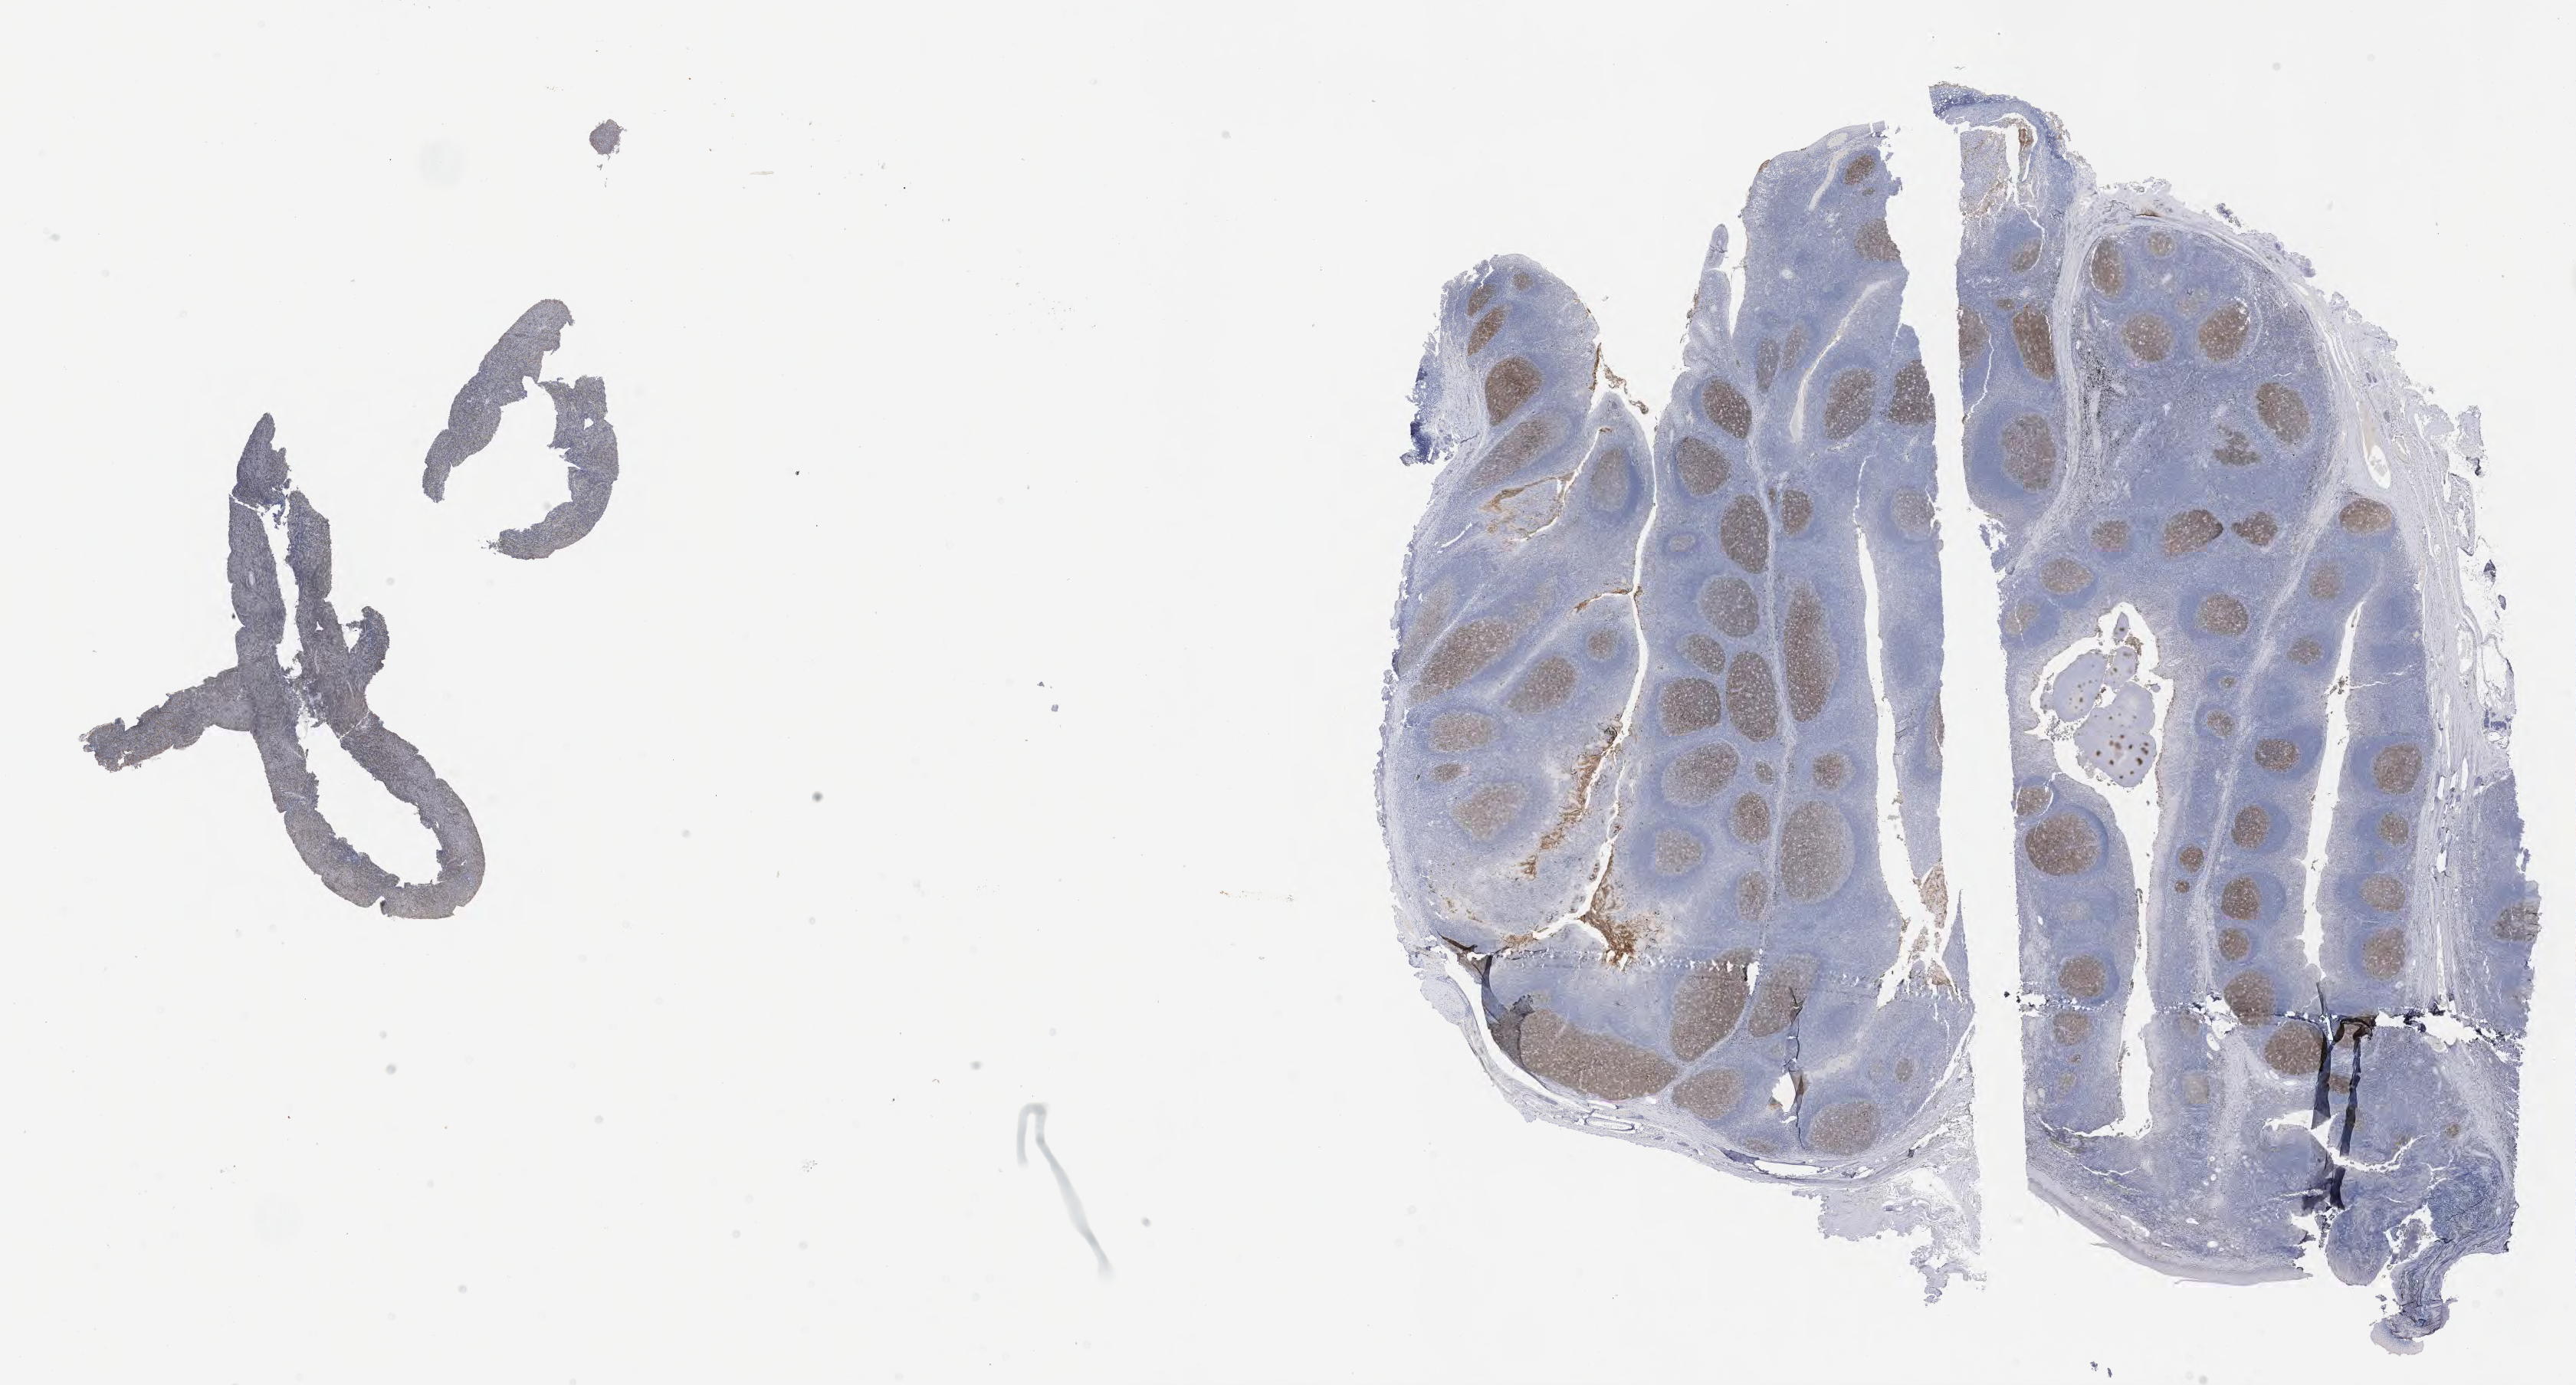
Whole-slide image, immunohistochemical stain for CD10 — shown as a low-resolution overview of the whole scanned area (about 27.2 x 14.6 mm). Patient male; aged 52.
- specimen: tumor tissue; anatomic site: liver